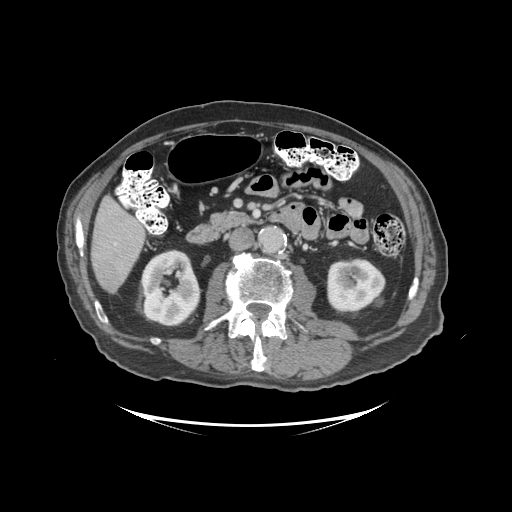
Contrast-enhanced abdominal CT (liver protocol), one axial slice; position 35 of 99 along the scan axis; reconstruction kernel STANDARD; soft-tissue window (W 400 / L 40 HU); 512 × 512 image matrix, field of view 460 × 460 mm. From the clinical record (not read from this slice): diagnosis: hepatocellular carcinoma (patient treated with transarterial chemoembolisation; whether this scan precedes or follows treatment is not stated here); TNM stage (as recorded): Stage-I; Child-Pugh class: A; tumour differentiation: moderately differentiated.
Structures marked on this image (semi-automatic segmentation, software-assisted and operator-edited):
- liver parenchyma outside the tumour (the mass and vessels are separate outlines, so this box may not span the whole liver): bounding box <90,196,144,294> (left, top, right, bottom; pixels)